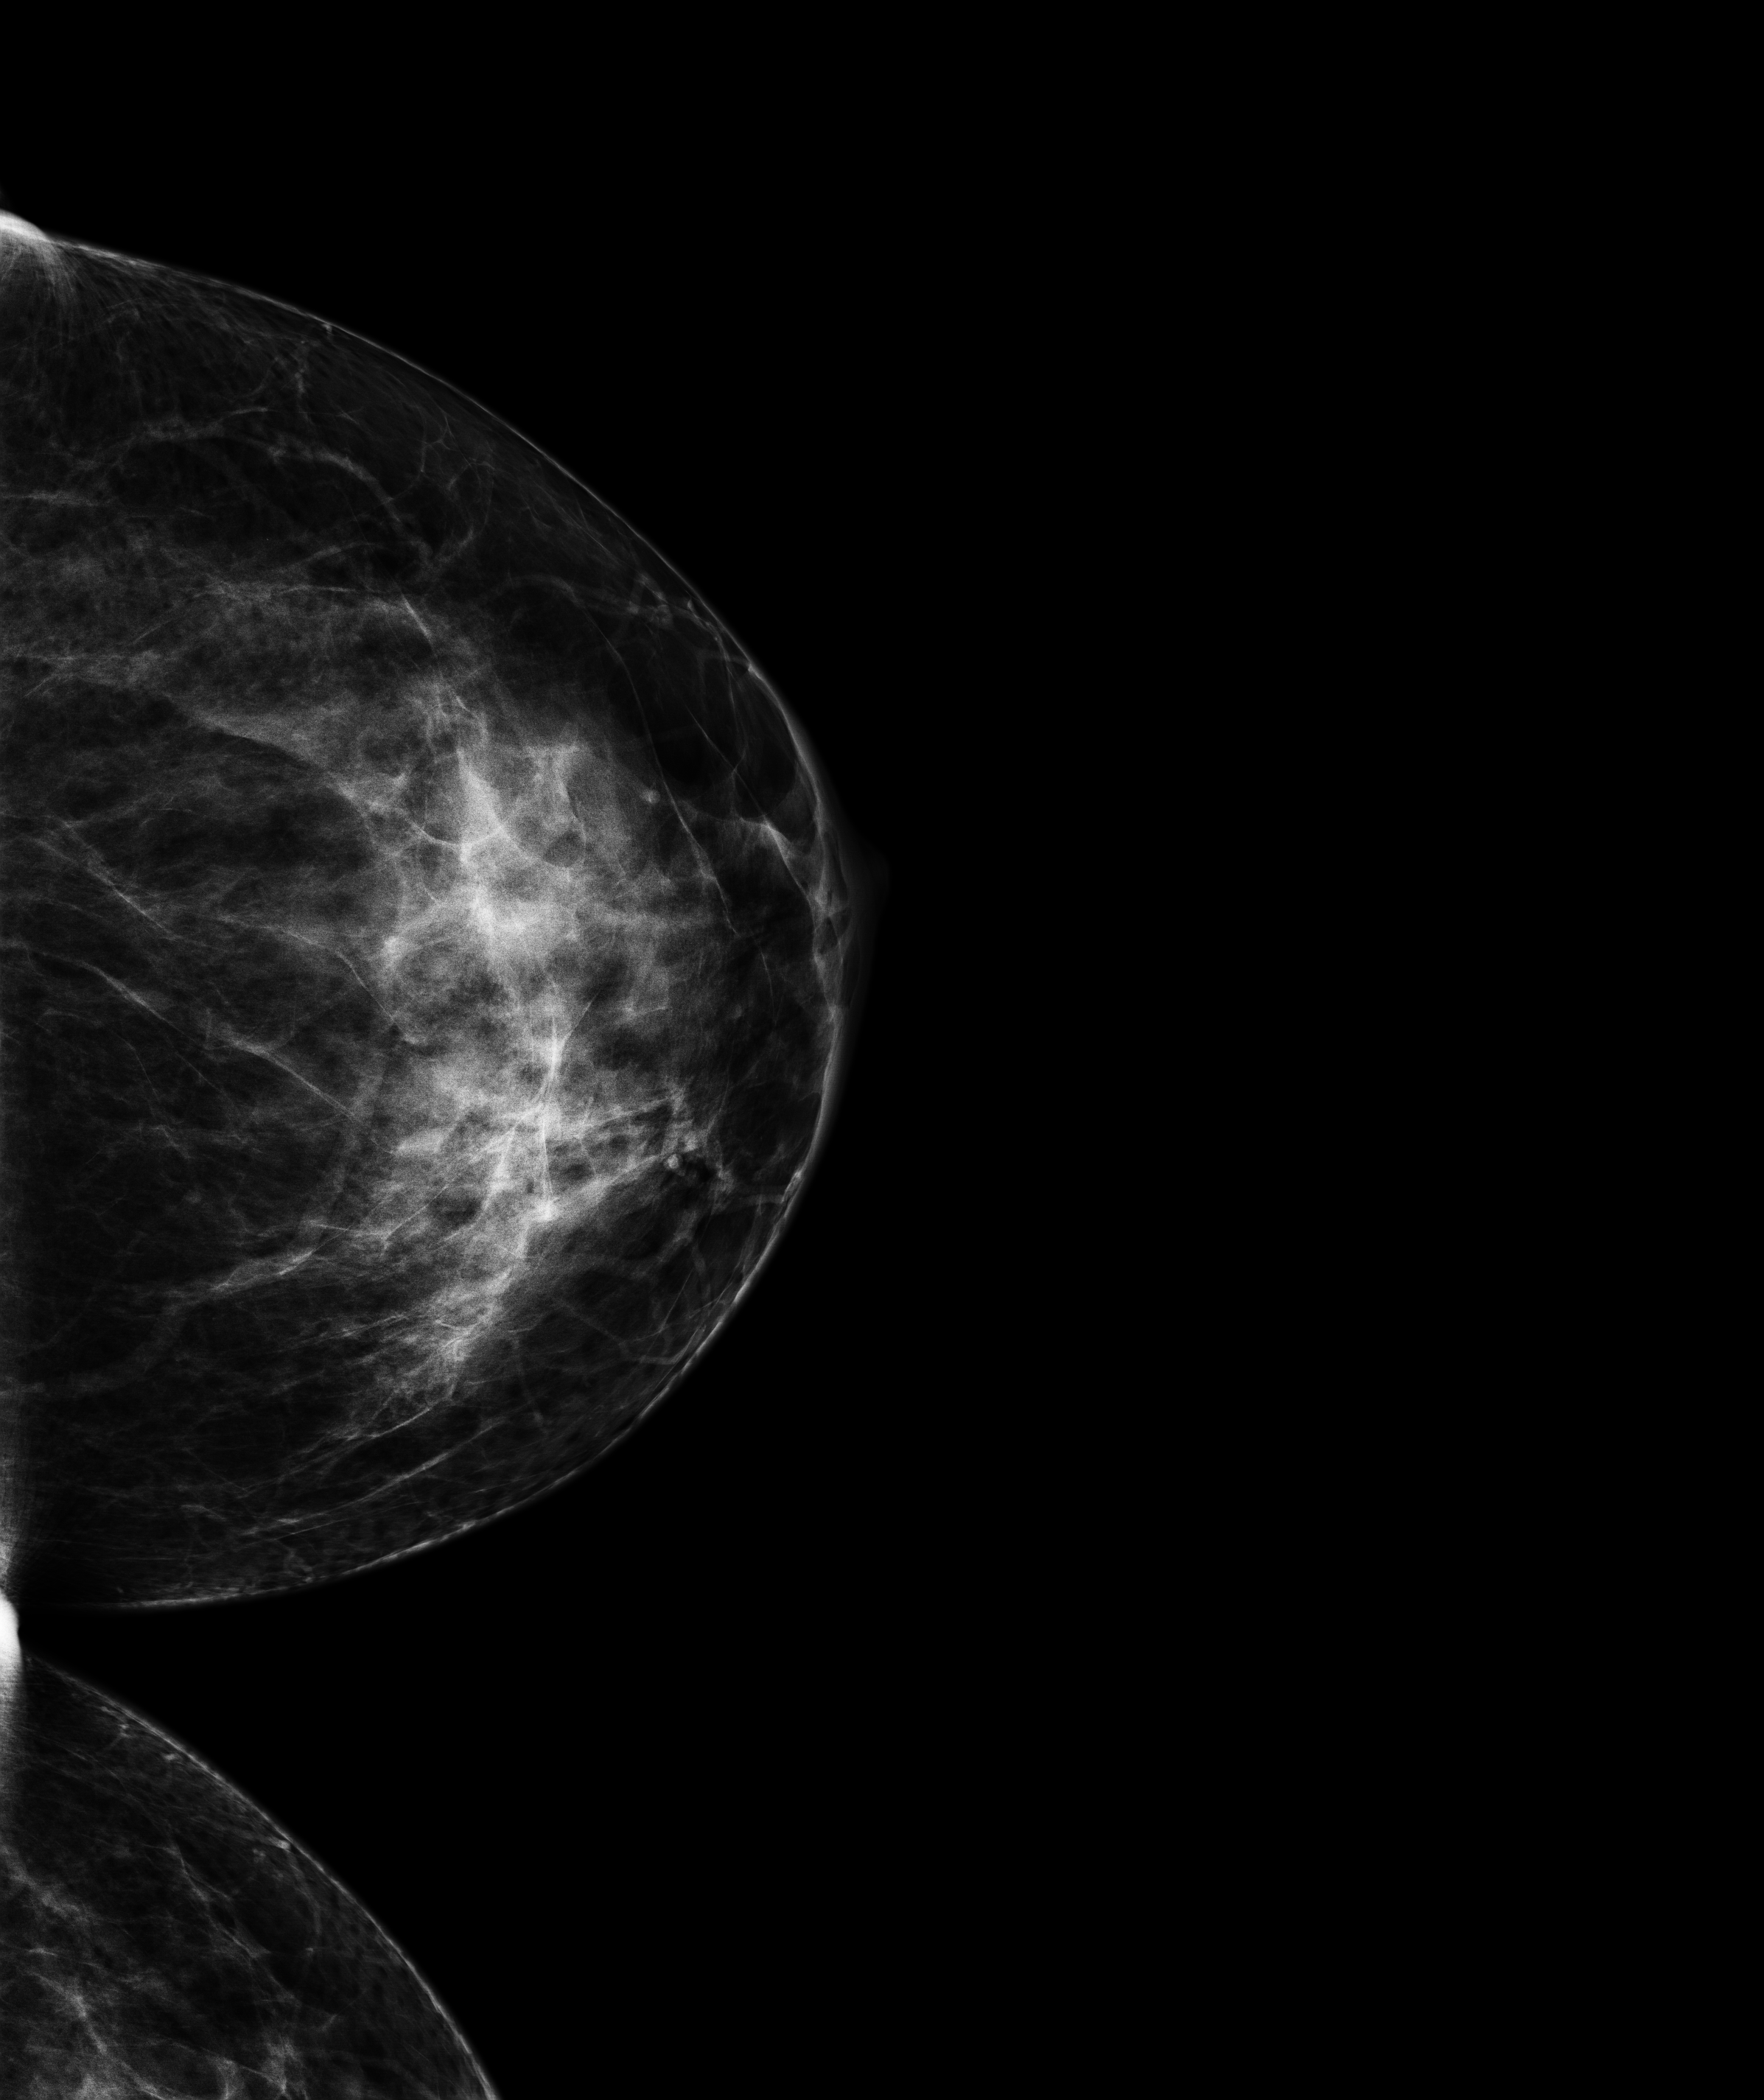
Screening examination, compressed breast thickness 74.1 mm. Patient: female, 45 years.
Image type: full-field digital mammogram. Breast: left. Projection: cranio-caudal projection.